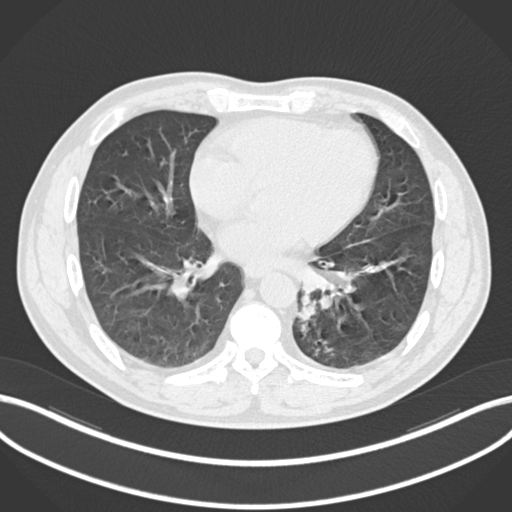
Chest CT, one axial slice; slice 84 of 223 in the series (ordered by position); lung window (W 1500 / L -600 HU); 512 × 512 image matrix, field of view 400 × 400 mm. Male patient, age 50 years. From the clinical record (not read from this slice): clinical TNM (as recorded): T2a N3 M0.
Annotated regions visible in this slice (bounding box drawn by a radiologist):
- lung tumour (recorded histology: squamous cell carcinoma): bounding box (x1, y1, x2, y2) in pixels: (296, 291, 318, 335)